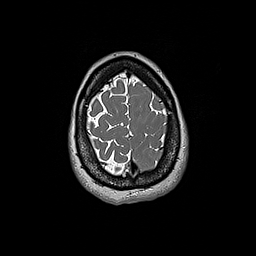
Brain MRI from a brain-tumour surgery series, one axial slice; slice 47 of 192 in the series (ordered by position); 1 mm slice thickness; 256 × 256 image matrix. From the clinical record (not read from this slice): histopathology: Glioblastoma; WHO grade: 4; IDH mutation: no.
Outlined on this slice (outlined manually by an expert reader):
- tumour: bounding box (x1, y1, x2, y2) in pixels: (160, 136, 166, 151)